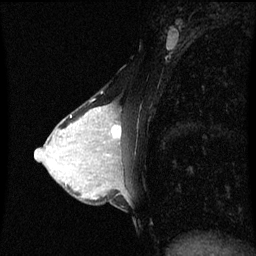
Breast MRI (dynamic contrast-enhanced), one sagittal slice. Position 32 of 60 along the scan axis. Dynamic contrast-enhanced series, image 2 of 3 at this slice position (ordered by acquisition). 1.5 T. TE 4.2 ms, TR 8.9 ms. 256 × 256 image matrix. Female patient, age 33 years. From the clinical record (not read from this slice): setting: breast cancer imaged before/during neoadjuvant chemotherapy; receptor status: HER2-positive.
Outlined on this slice (semi-automatically segmented with operator editing):
- analysis volume of interest (the breast-tissue region the enhancement analysis was run in; not a lesion): bounding box <95,106,124,153> (left, top, right, bottom; pixels)
- tumour enhancement mask (voxels above the 70 % enhancement threshold inside the analysis volume of interest): <112,126,121,139>